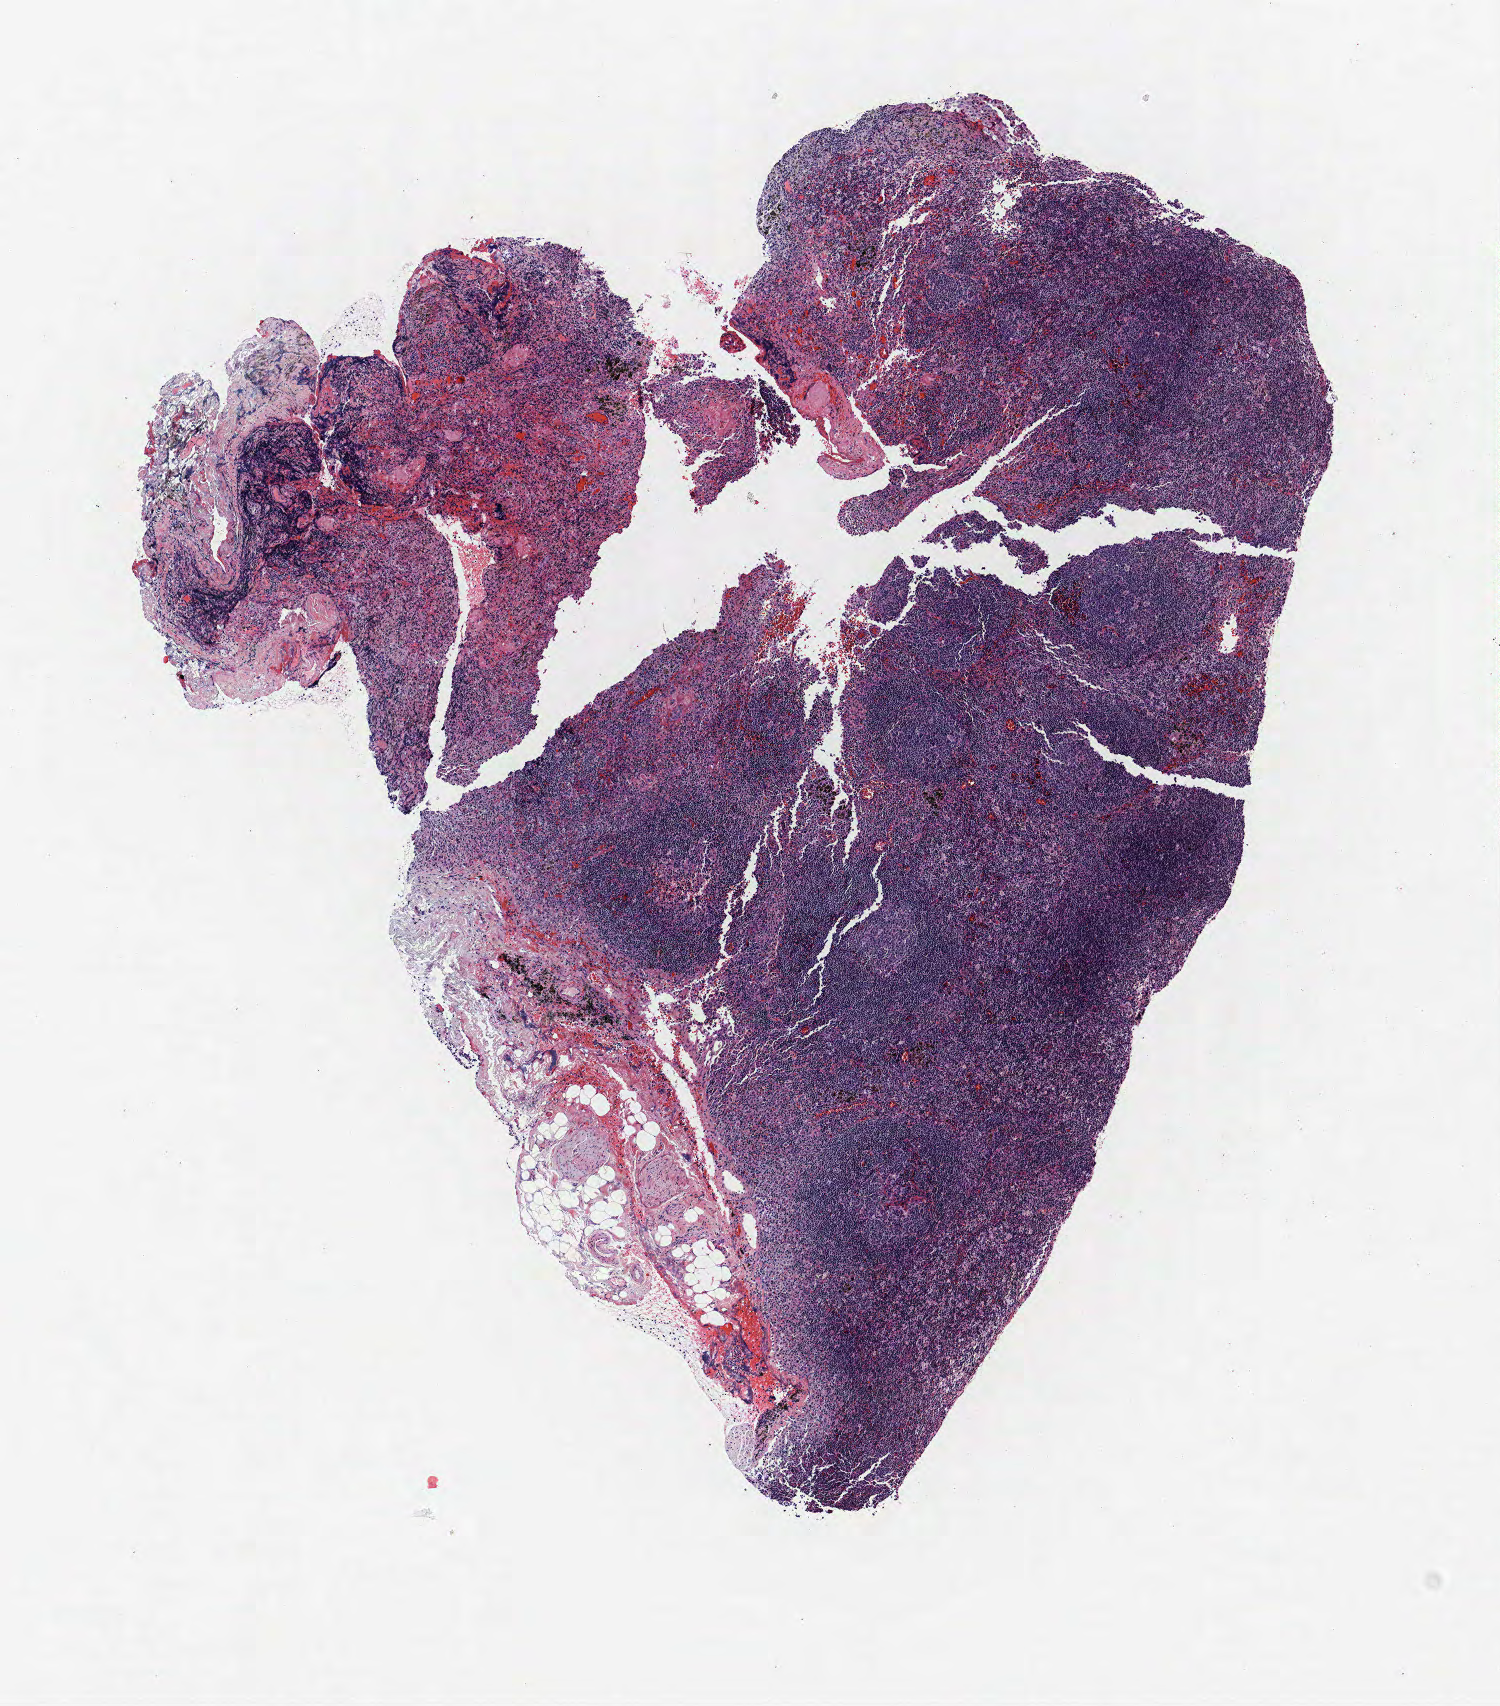
Whole-slide histology image, H&E-stained — whole scanned area (about 6.0 x 6.8 mm, acquisition: 40x scan) shown as a low-resolution overview, FFPE section, lung tissue. Male patient, aged 59 at enrolment. Grade: poorly differentiated (G3).
Tumour size (pathology): 34 mm. Stage (AJCC 6th edition): IIIA. Participant's lung-cancer diagnosis: Large cell carcinoma, NOS (ICD-O-3 8012/3). Primary tumour location (clinical record): right upper lobe.